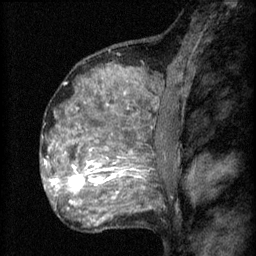
Breast MRI (dynamic contrast-enhanced), one sagittal slice; slice 41 of 60 in the series (ordered by position); 3 images stored at this slice position (order not interpretable as contrast timing); 1.5 T; TE 4.2 ms, TR 8.2 ms; 2 mm slice thickness; 256 × 256 image matrix, field of view 180 × 180 mm. Female patient, age 48 years.
Outlined on this slice (semi-automatic segmentation, software-assisted and operator-edited):
- analysis volume of interest (the breast-tissue region the enhancement analysis was run in; not a lesion): bounding box <61,138,149,201> (left, top, right, bottom; pixels)
- tumour enhancement mask (voxels above the 70 % enhancement threshold inside the analysis volume of interest): <67,166,119,195>